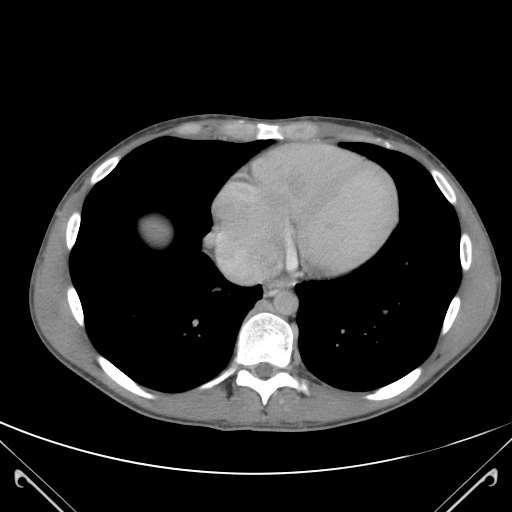
Contrast-enhanced abdominal CT (liver protocol), one axial slice; slice 112 of 118 in the series (ordered by position); 120 kVp; soft-tissue window (W 400 / L 40 HU); 512 × 512 image matrix, field of view 380 × 380 mm. Case-level facts recorded for this patient, not image findings: diagnosis: hepatocellular carcinoma (patient treated with transarterial chemoembolisation; whether this scan precedes or follows treatment is not stated here); TNM stage (as recorded): Stage-IIIB; Child-Pugh class: A; tumour nodularity: uninodular.
Outlined on this slice (semi-automatically segmented with operator editing):
- abdominal aorta: bounding box <274,291,298,314> (left, top, right, bottom; pixels)